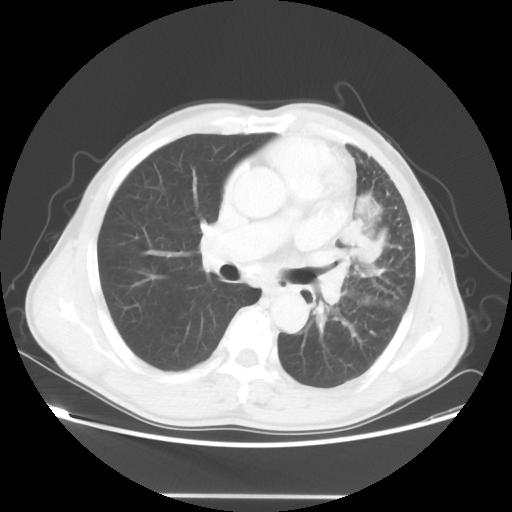
Chest CT, one axial slice. Slice 29 of 55 in the series (ordered by position). 100 kVp. Lung window (W 1500 / L -600 HU). 5 mm slice thickness. 512 × 512 image matrix, field of view 398 × 398 mm. Male patient, age 60 years. Case-level facts recorded for this patient, not image findings: clinical TNM (as recorded): T3 N3 M0.
Outlined on this slice (bounding box drawn by a radiologist):
- lung tumour (recorded histology: adenocarcinoma): bounding box [x1, y1, x2, y2] px = [340, 210, 389, 276]